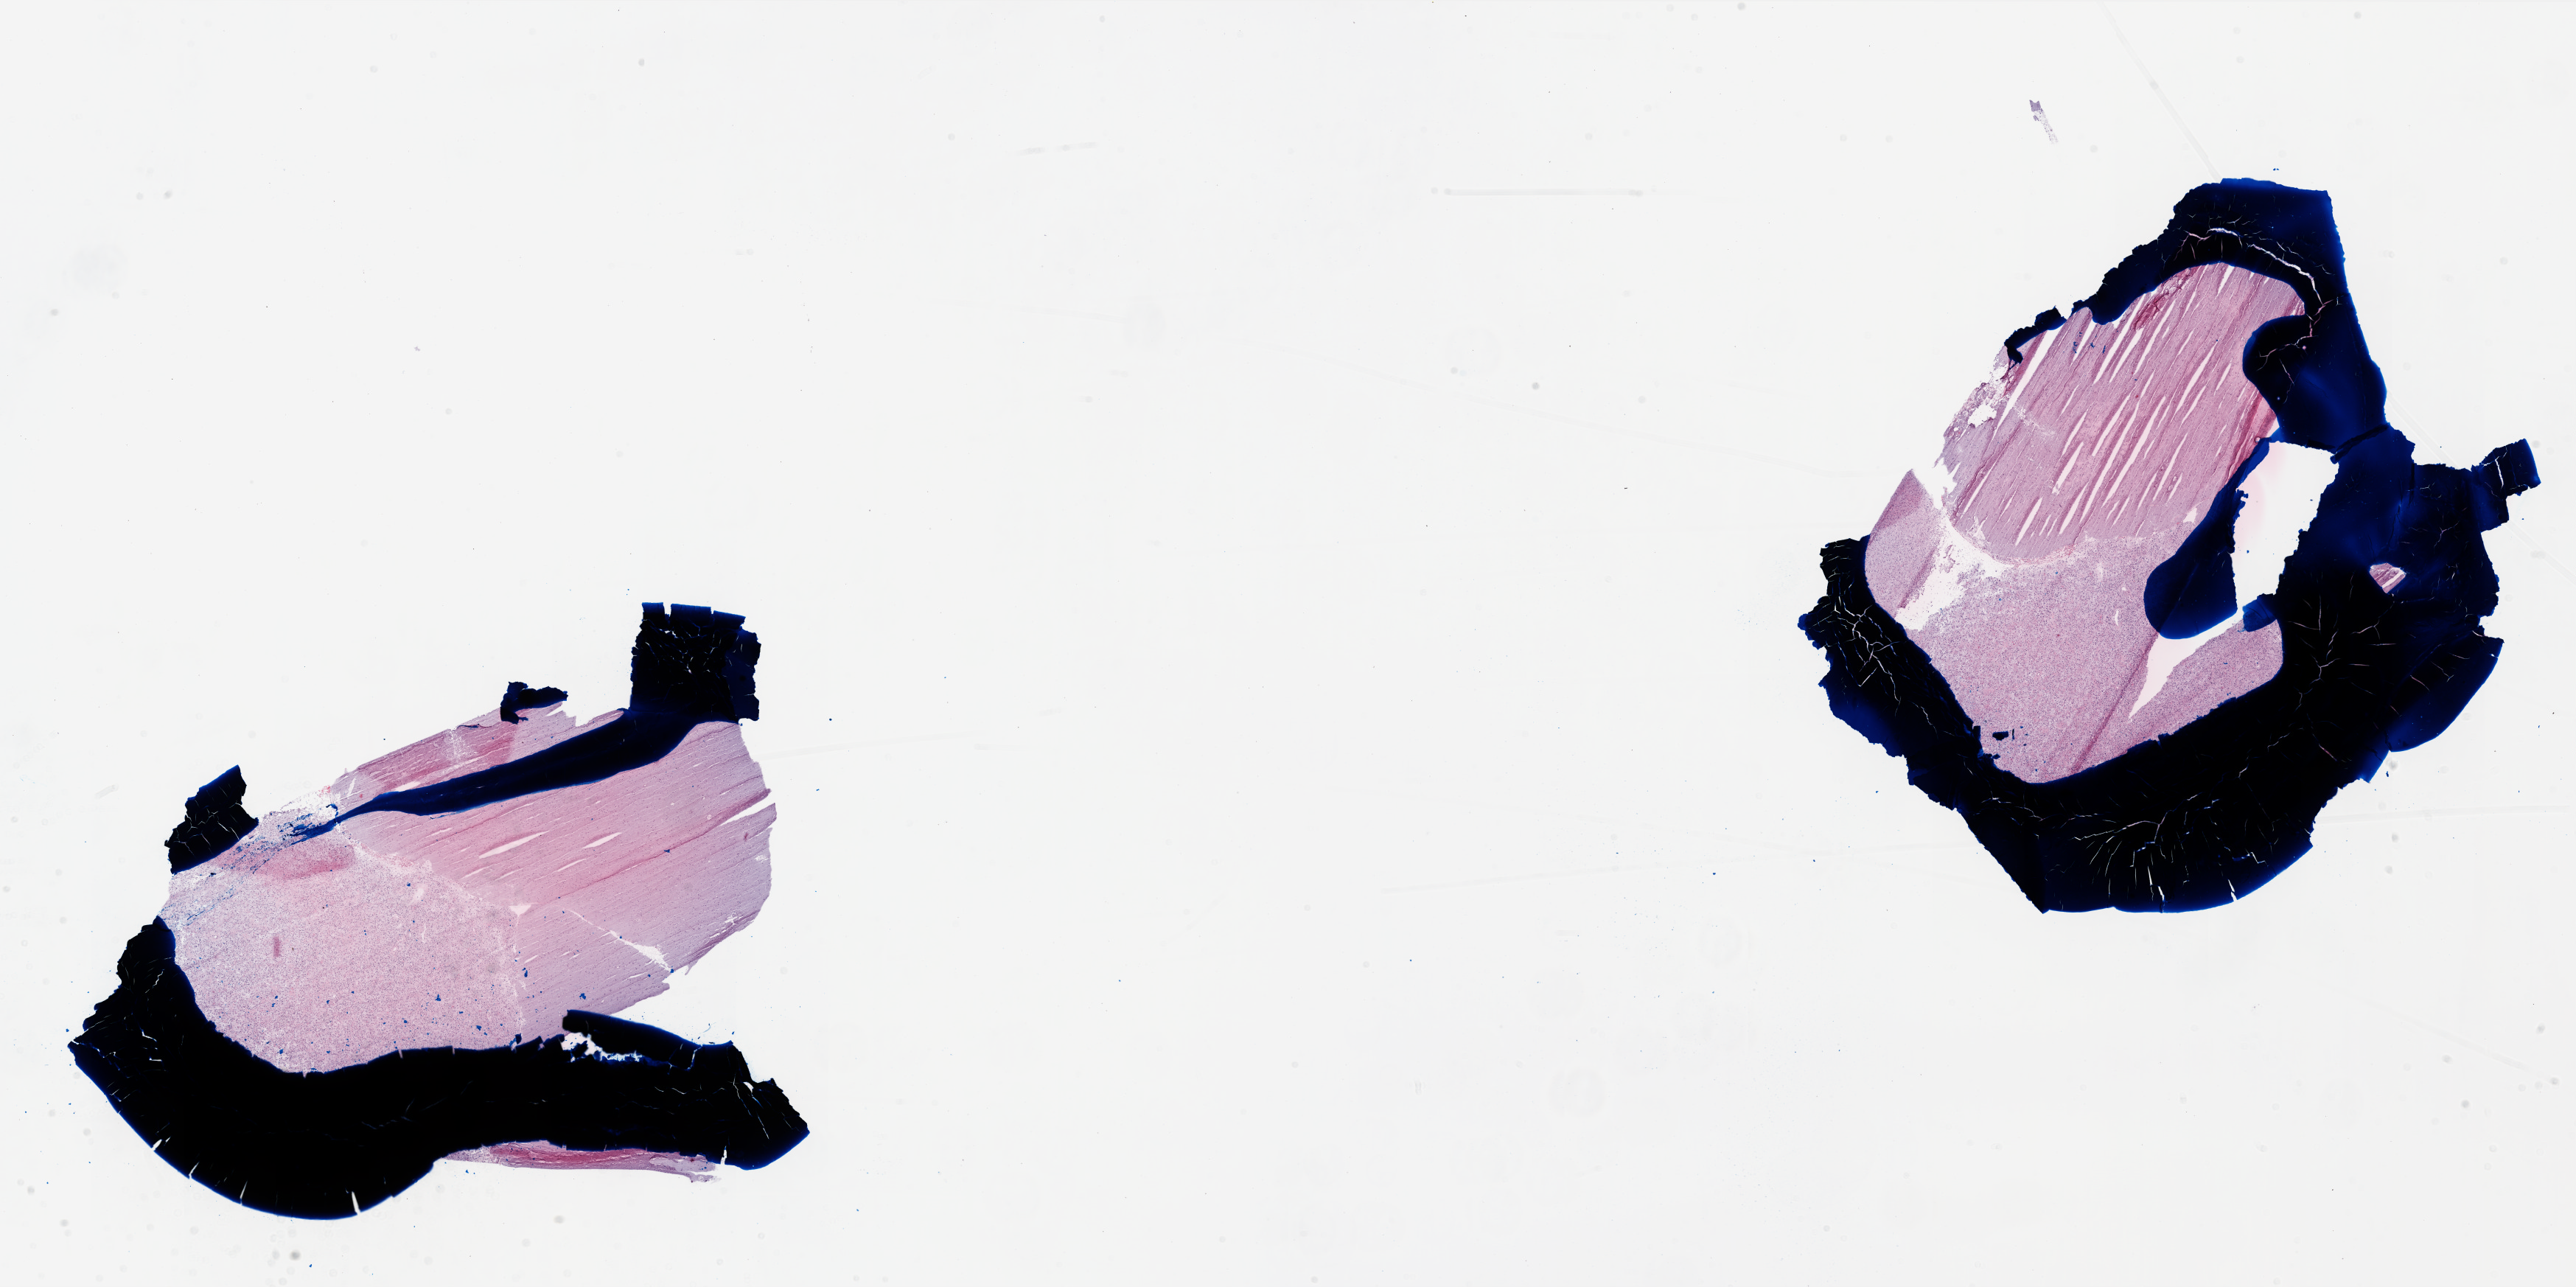
H&E-stained whole-slide image, shown as a low-resolution overview of the whole scanned area (about 28.0 x 14.0 mm, from a 20x scan), frozen section from the top of the tissue portion, primary tumour sample from the brain. Male patient; age at initial diagnosis 31 years. Pathologist review of this section (percent, as recorded): tumour cells 50%, tumour nuclei 80%, normal cells 50%, stromal cells 0%, necrosis 0%.
* histologic diagnosis: Glioblastoma